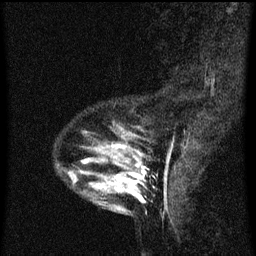
Breast MRI (dynamic contrast-enhanced), one sagittal slice. Position 15 of 60 along the scan axis. Dynamic contrast-enhanced series, image 2 of 3 at this slice position (ordered by acquisition). 1.5 T. TE 4.2 ms, TR 8 ms. 2 mm slice thickness. 256 × 256 image matrix, field of view 180 × 180 mm. Female patient, age 33 years.
Outlined on this slice (semi-automatically segmented with operator editing):
- analysis volume of interest (the breast-tissue region the enhancement analysis was run in; not a lesion): bounding box <61,130,146,213> (left, top, right, bottom; pixels)
- tumour enhancement mask (voxels above the 70 % enhancement threshold inside the analysis volume of interest): <83,144,144,197>